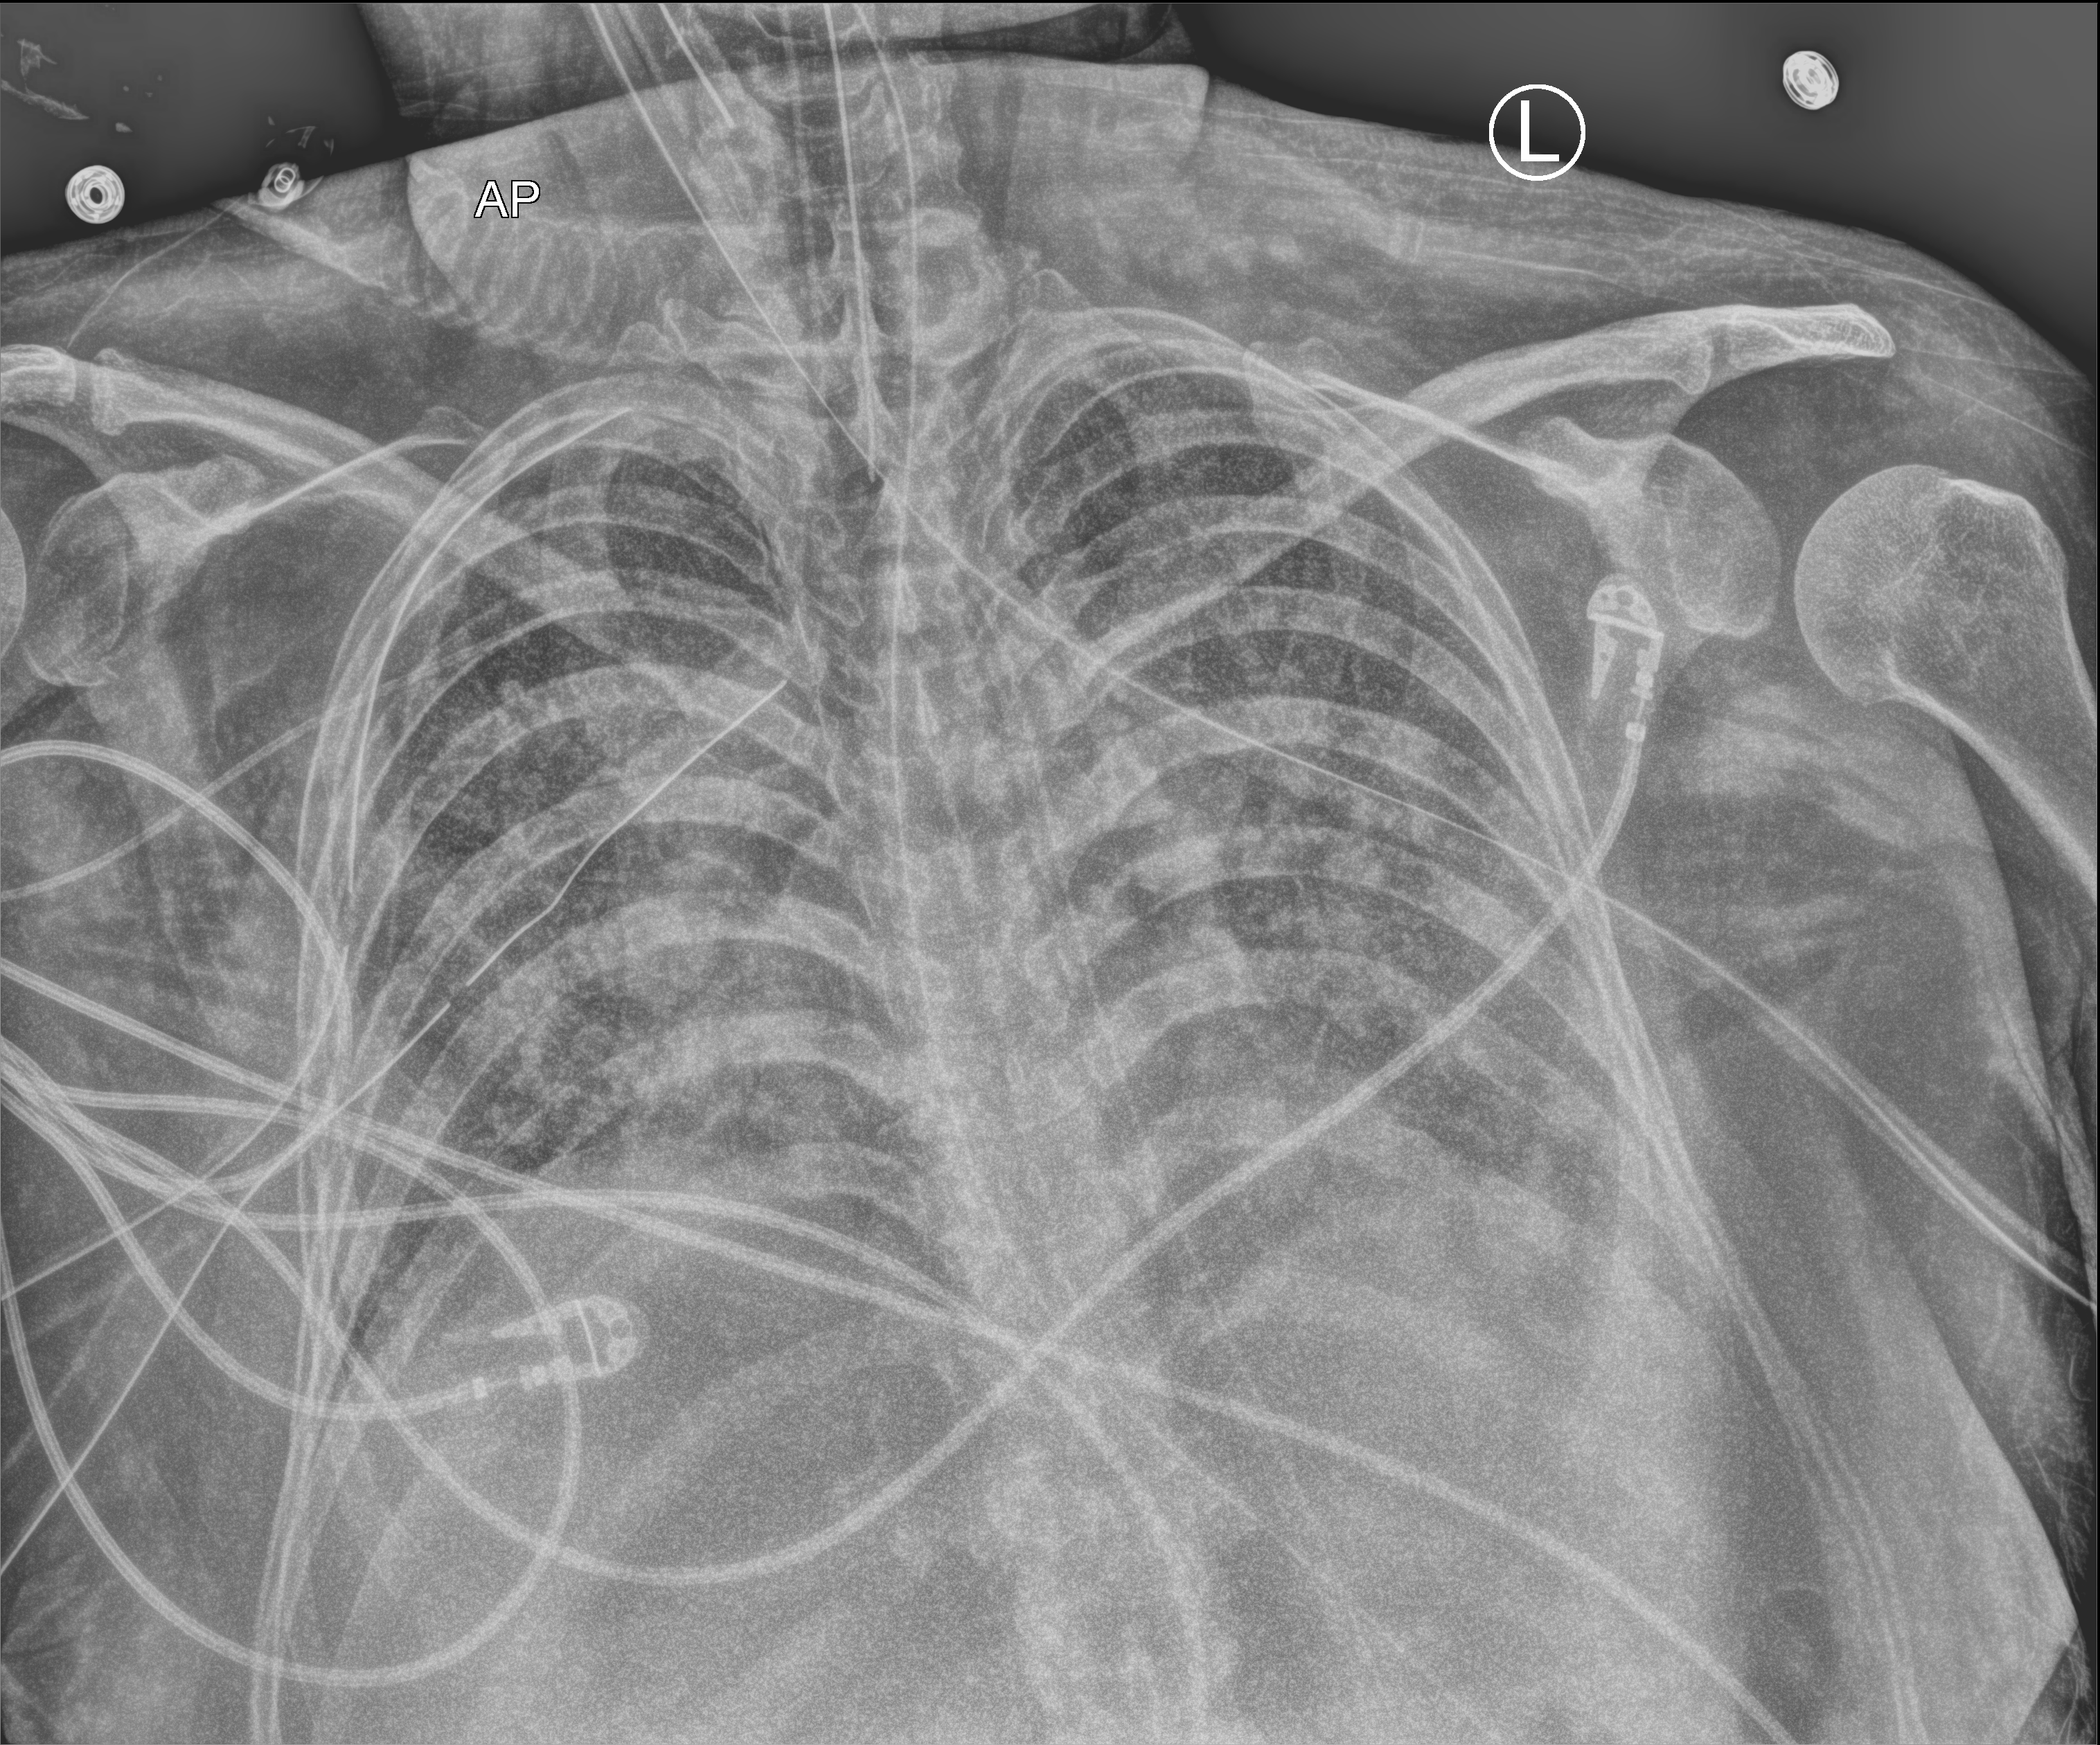
Bedside chest radiograph (computed radiography), anteroposterior (AP) projection. Adult patient hospitalised with COVID-19, age 18–59 years.
From the hospital-stay record, not from the radiograph (when in the stay this image was taken is not recorded):
- admitted to intensive care during this hospital stay: yes